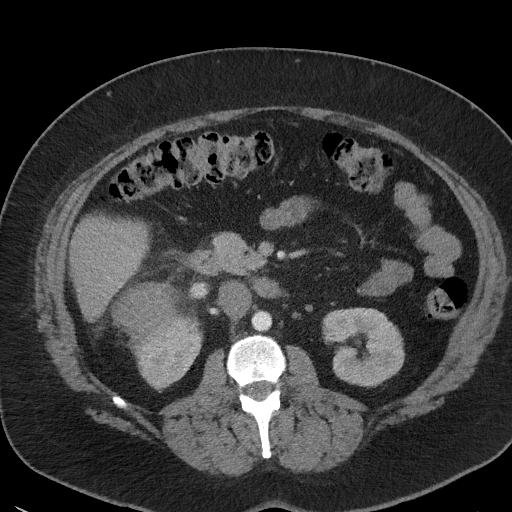
Contrast-enhanced abdominal CT, one axial slice. Position 20 of 56 along the scan axis. 120 kVp. Intravenous contrast given. Soft-tissue window (W 400 / L 40 HU). 512 × 512 image matrix. Female patient, age 35 years. Case-level facts recorded for this patient, not image findings: diagnosis: adrenocortical carcinoma; tumour side: right adrenal; tumour size at pathology: 15 cm; Ki-67 index: 40 %; stage (as recorded): 2.
Structures marked on this image (semi-automatically segmented with operator editing):
- mass: box from (x=115, y=285) to (x=178, y=341) px